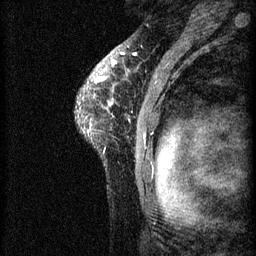
Breast MRI (dynamic contrast-enhanced), one sagittal slice; slice 50 of 60 in the series (ordered by position); 3 images stored at this slice position (order not interpretable as contrast timing); 1.5 T; TE 4.2 ms, TR 8.2 ms; 2 mm slice thickness; 256 × 256 image matrix, field of view 180 × 180 mm. Patient: female, 41 years.
Annotated regions visible in this slice (semi-automatic segmentation, software-assisted and operator-edited):
- analysis volume of interest (the breast-tissue region the enhancement analysis was run in; not a lesion): bounding box [x1, y1, x2, y2] px = [76, 62, 160, 175]
- tumour enhancement mask (voxels above the 70 % enhancement threshold inside the analysis volume of interest): [87, 62, 117, 133]